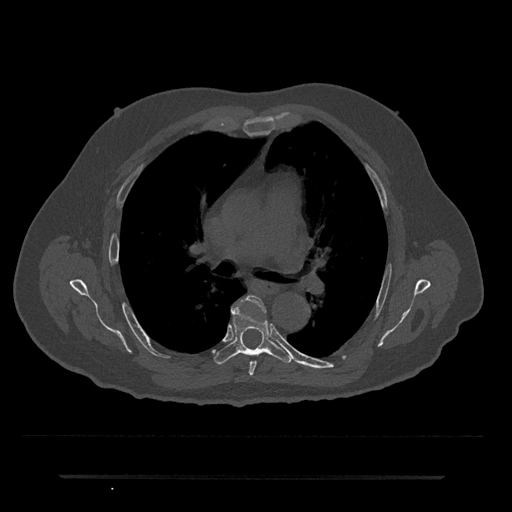
CT including the spine, one axial slice; reconstruction kernel Br40s/3; bone window (W 1800 / L 400 HU); 0.5 mm slice thickness; 512 × 512 image matrix. Male patient, age 69 years. From the clinical record (not read from this slice): primary cancer: prostate.
Structures marked on this image (semi-automatically segmented with operator editing):
- T5 vertebra: box from (x=246, y=296) to (x=266, y=376) px
- T6 vertebra: (x=214, y=303)–(x=293, y=364)